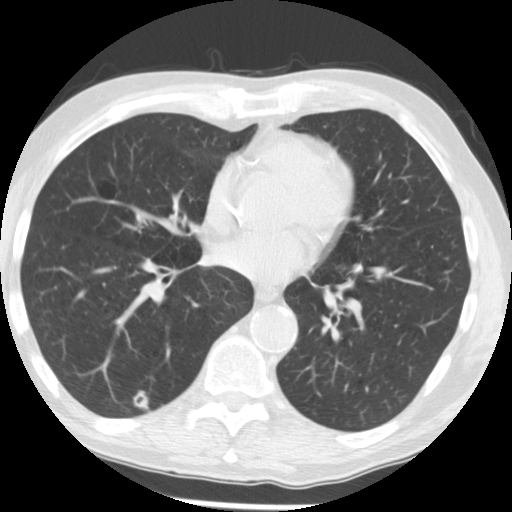
Axial slice from a low-dose chest CT screening exam. Second screening round (one year after baseline). Lung window (W 1500 / L -600 HU). 120 kVp. Slice 93 of 173 in the series. 512 × 512 image matrix. Male, age 62 years at enrolment. Current smoker at enrolment.
Expert reader's lesion annotation, bounding box <126,385,163,417> (left, top, right, bottom; pixels). The screening reader recorded 2 non-calcified nodules or masses ≥4 mm on this exam (right lower lobe, right lower lobe); which of them this box marks is not recorded. Lung cancer was diagnosed 506 days after this screen (after the third annual screen): adenocarcinoma, NOS, right lower lobe, moderately differentiated (G2), stage IIIB (AJCC 6th edition), 15 mm at pathology.